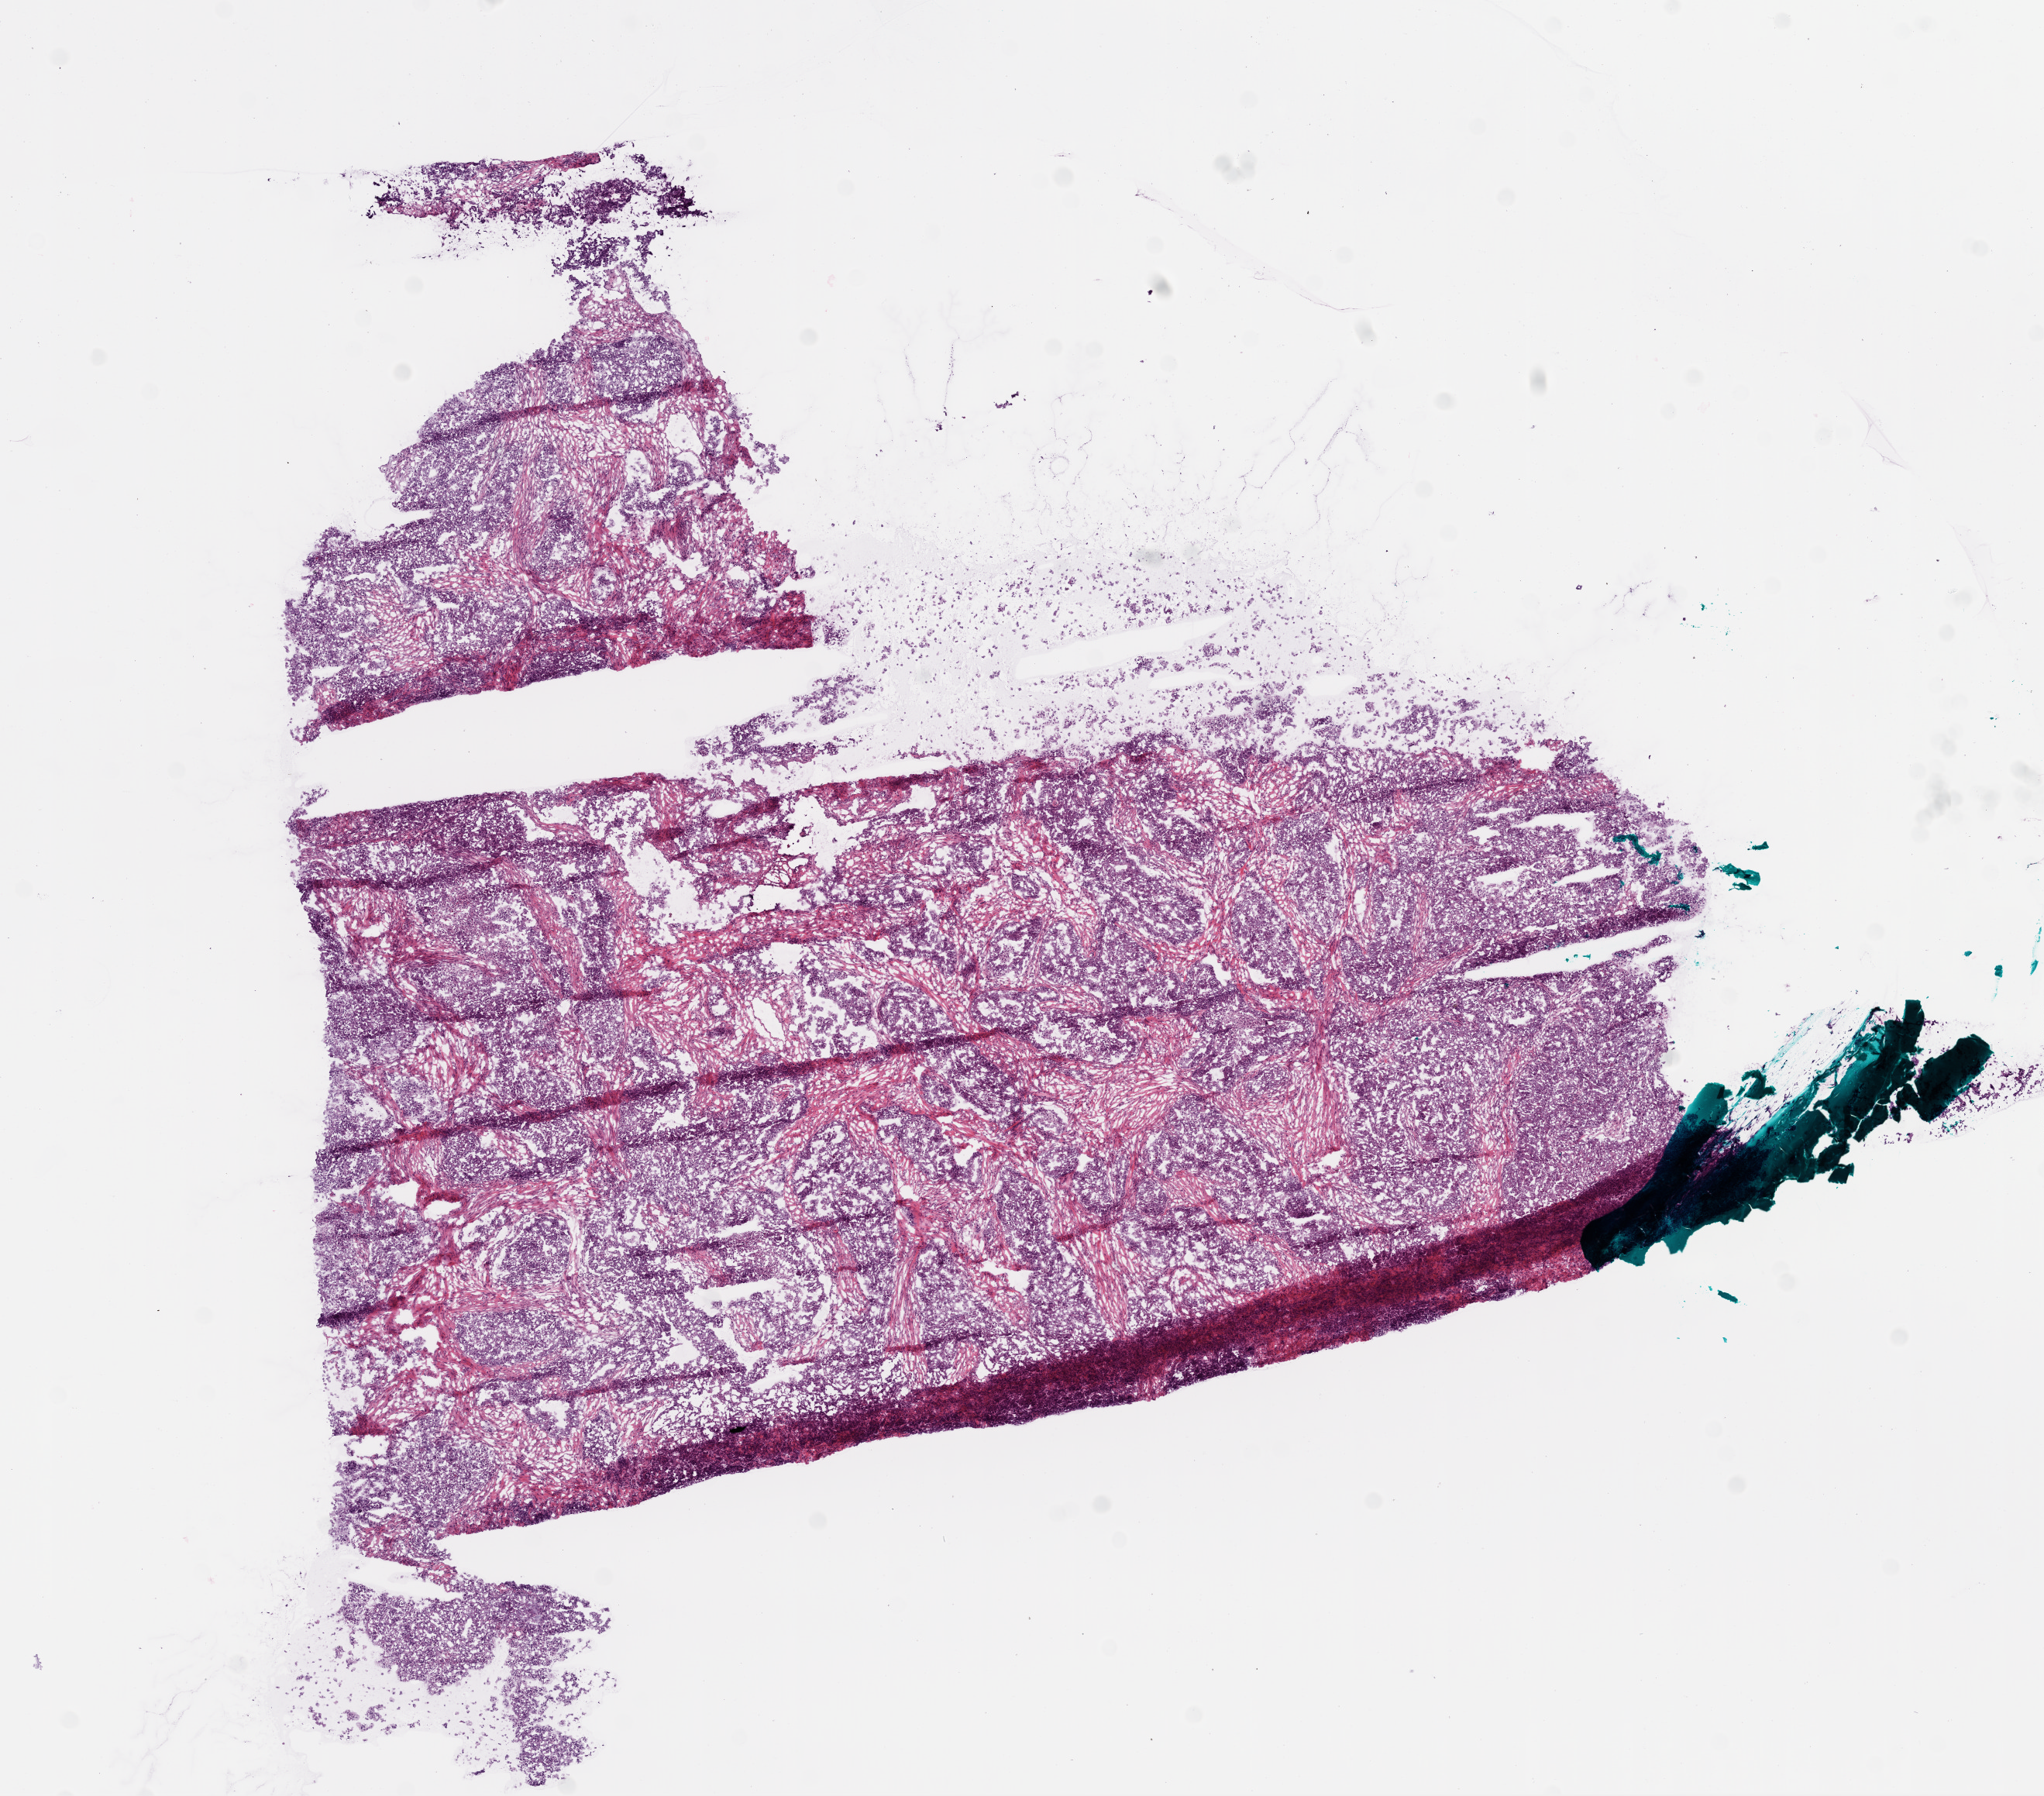
Hematoxylin and eosin (H&E) stained whole-slide image, a low-resolution overview of the entire scanned area, about 10.6 x 9.3 mm; frozen section; ovary, primary tumour sample. Female, age 73 years at initial diagnosis. Slide review estimates, as recorded: tumour cells 69%, tumour nuclei 80%.
Histologic diagnosis: Serous cystadenocarcinoma, NOS.